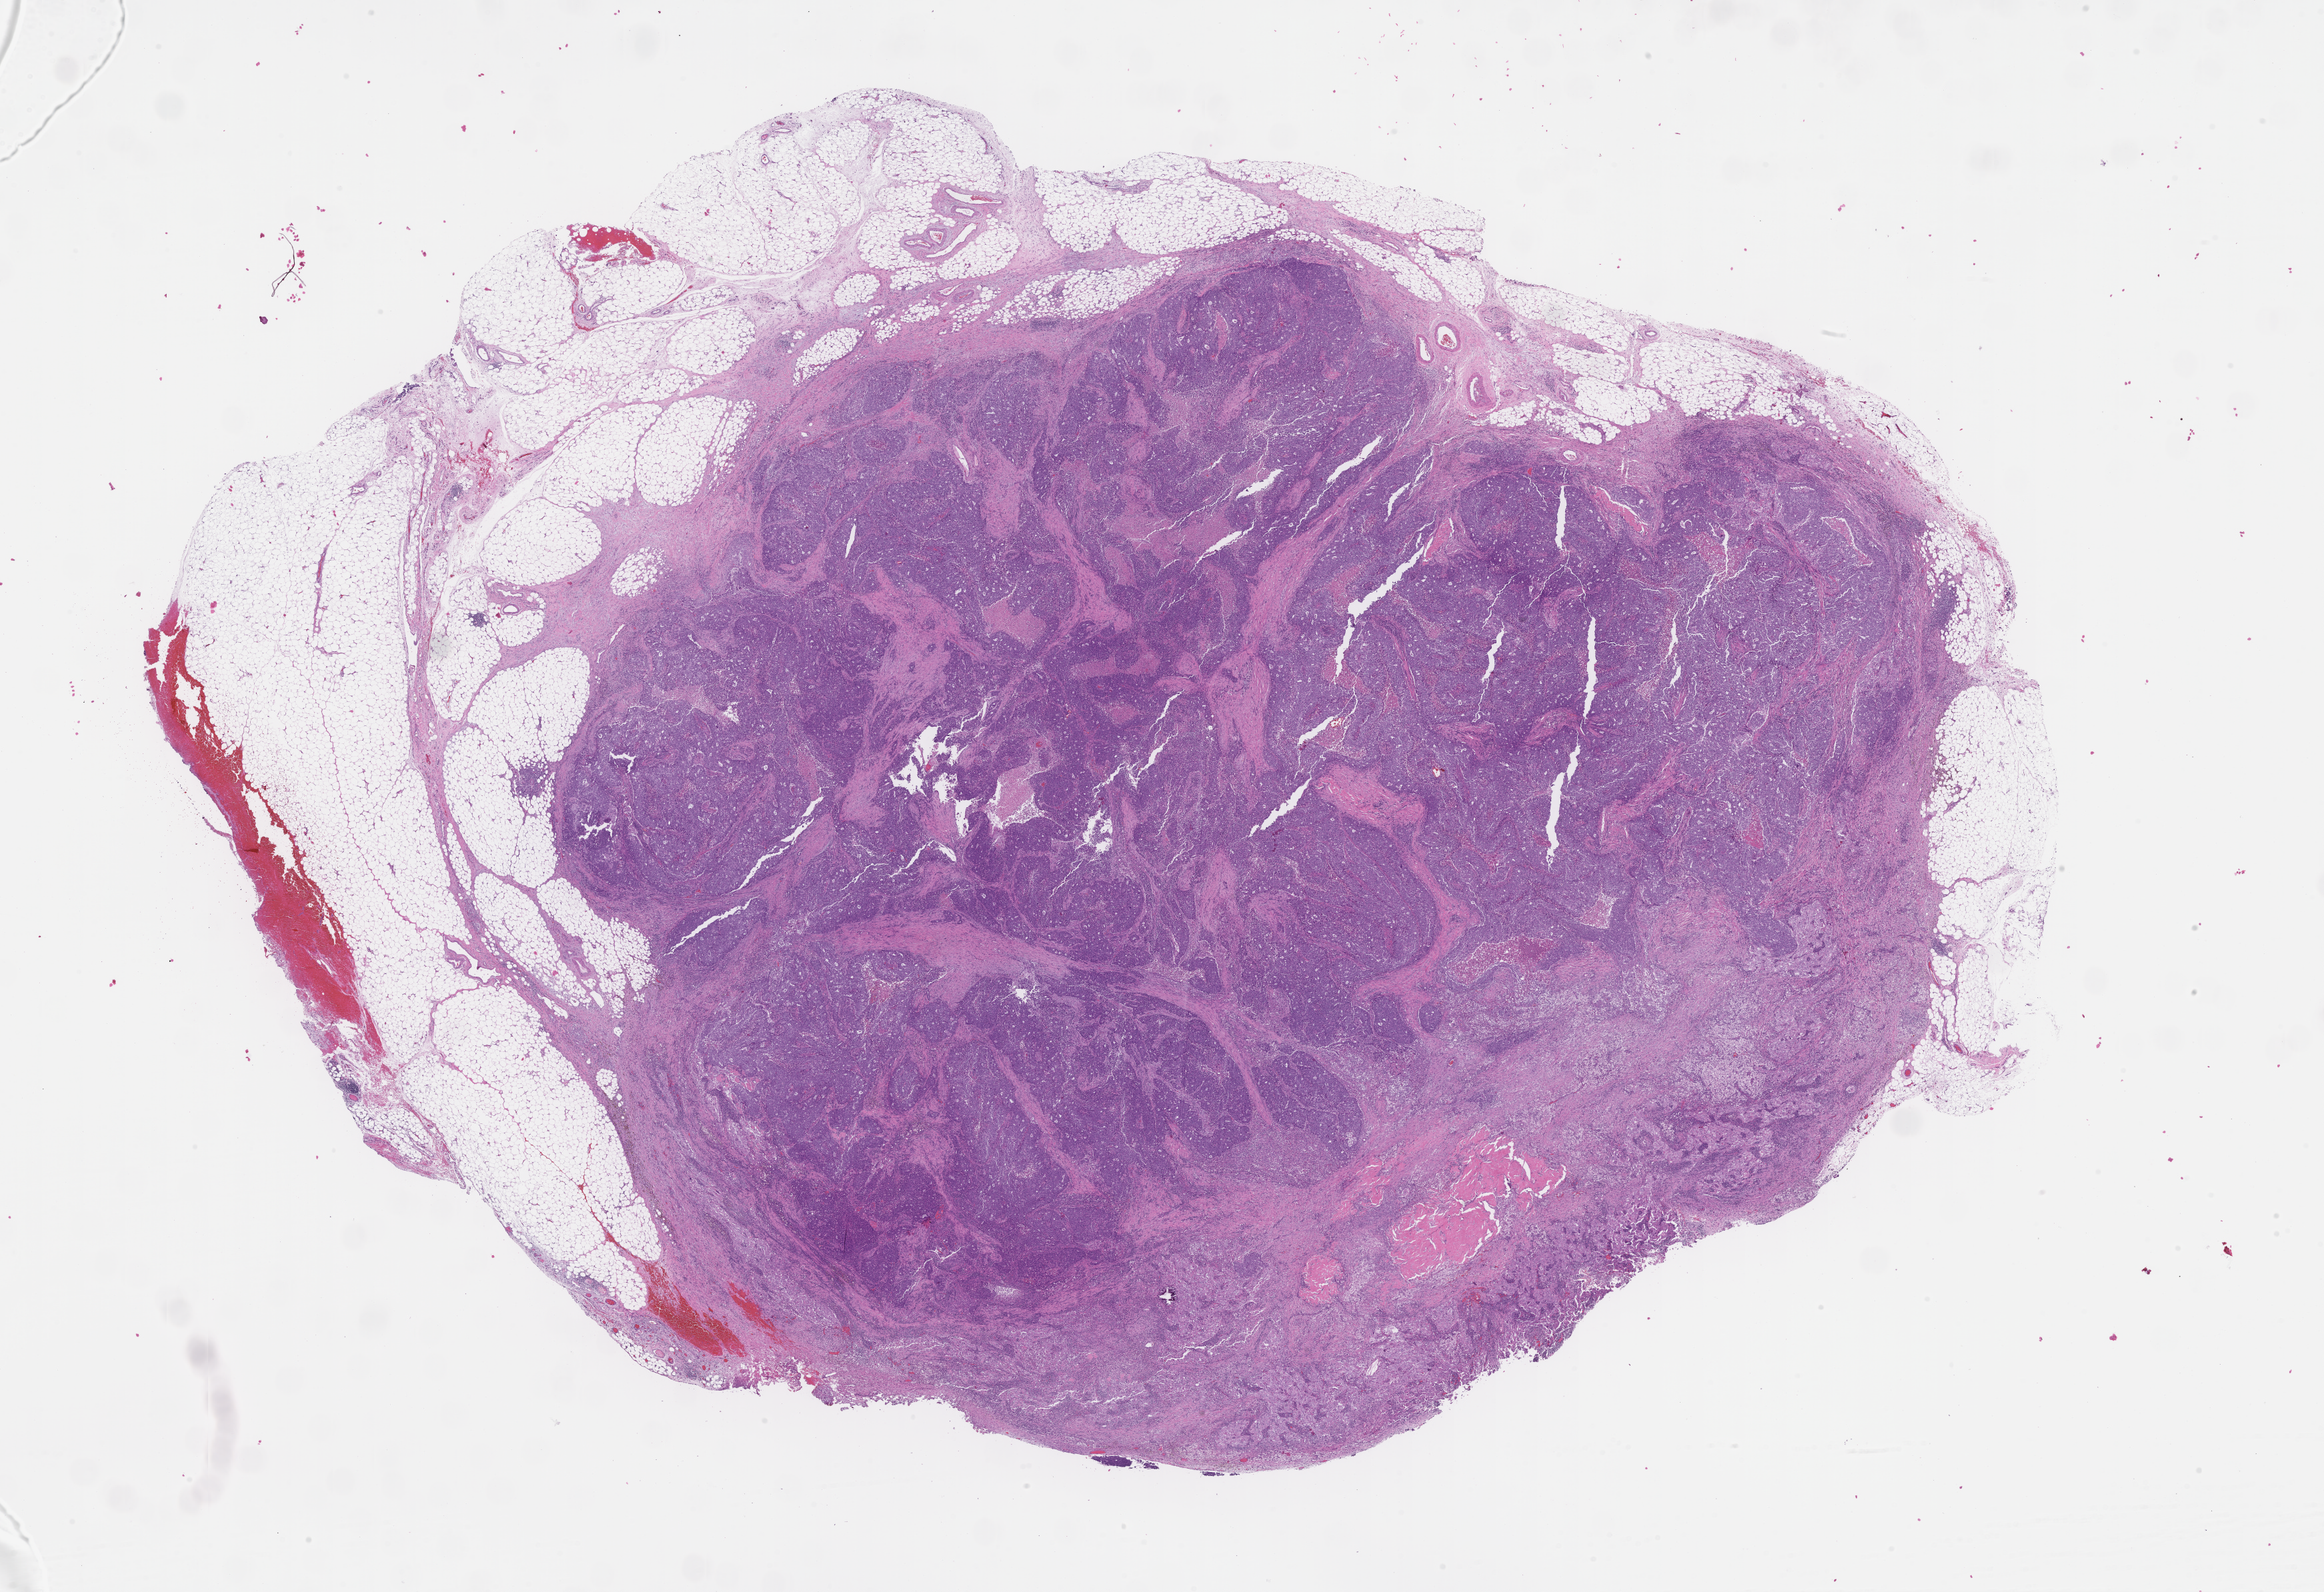
Whole-slide image, H&E stain — shown as a low-resolution overview of the whole scanned area (about 28.1 x 19.3 mm); formalin-fixed, paraffin-embedded (FFPE) tissue; tissue site: omentum; archival tissue. Patient sex: female.
This section: primary tumor. Diagnosis: Ovarian Carcinoma.